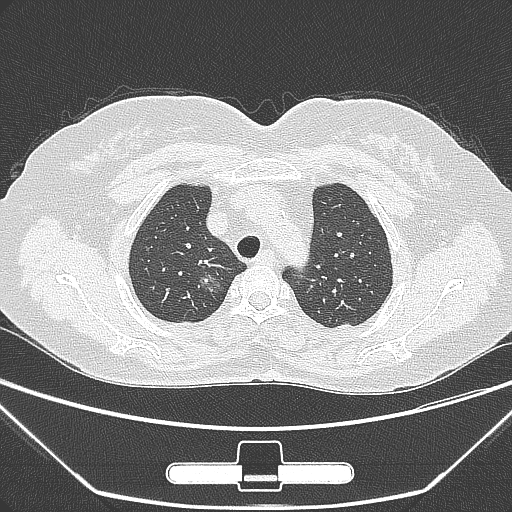
Chest CT, one axial slice; position 227 of 275 along the scan axis; 120 kVp; lung window (W 1500 / L -600 HU); 1 mm slice thickness; 512 × 512 image matrix, field of view 356 × 356 mm. Patient: female, 63 years. Case-level facts recorded for this patient, not image findings: clinical TNM (as recorded): T1a N0 M0; histopathological grade: G1.
Outlined on this slice (bounding box drawn by a radiologist):
- lung tumour (recorded histology: adenocarcinoma): box from (x=195, y=265) to (x=228, y=306) px